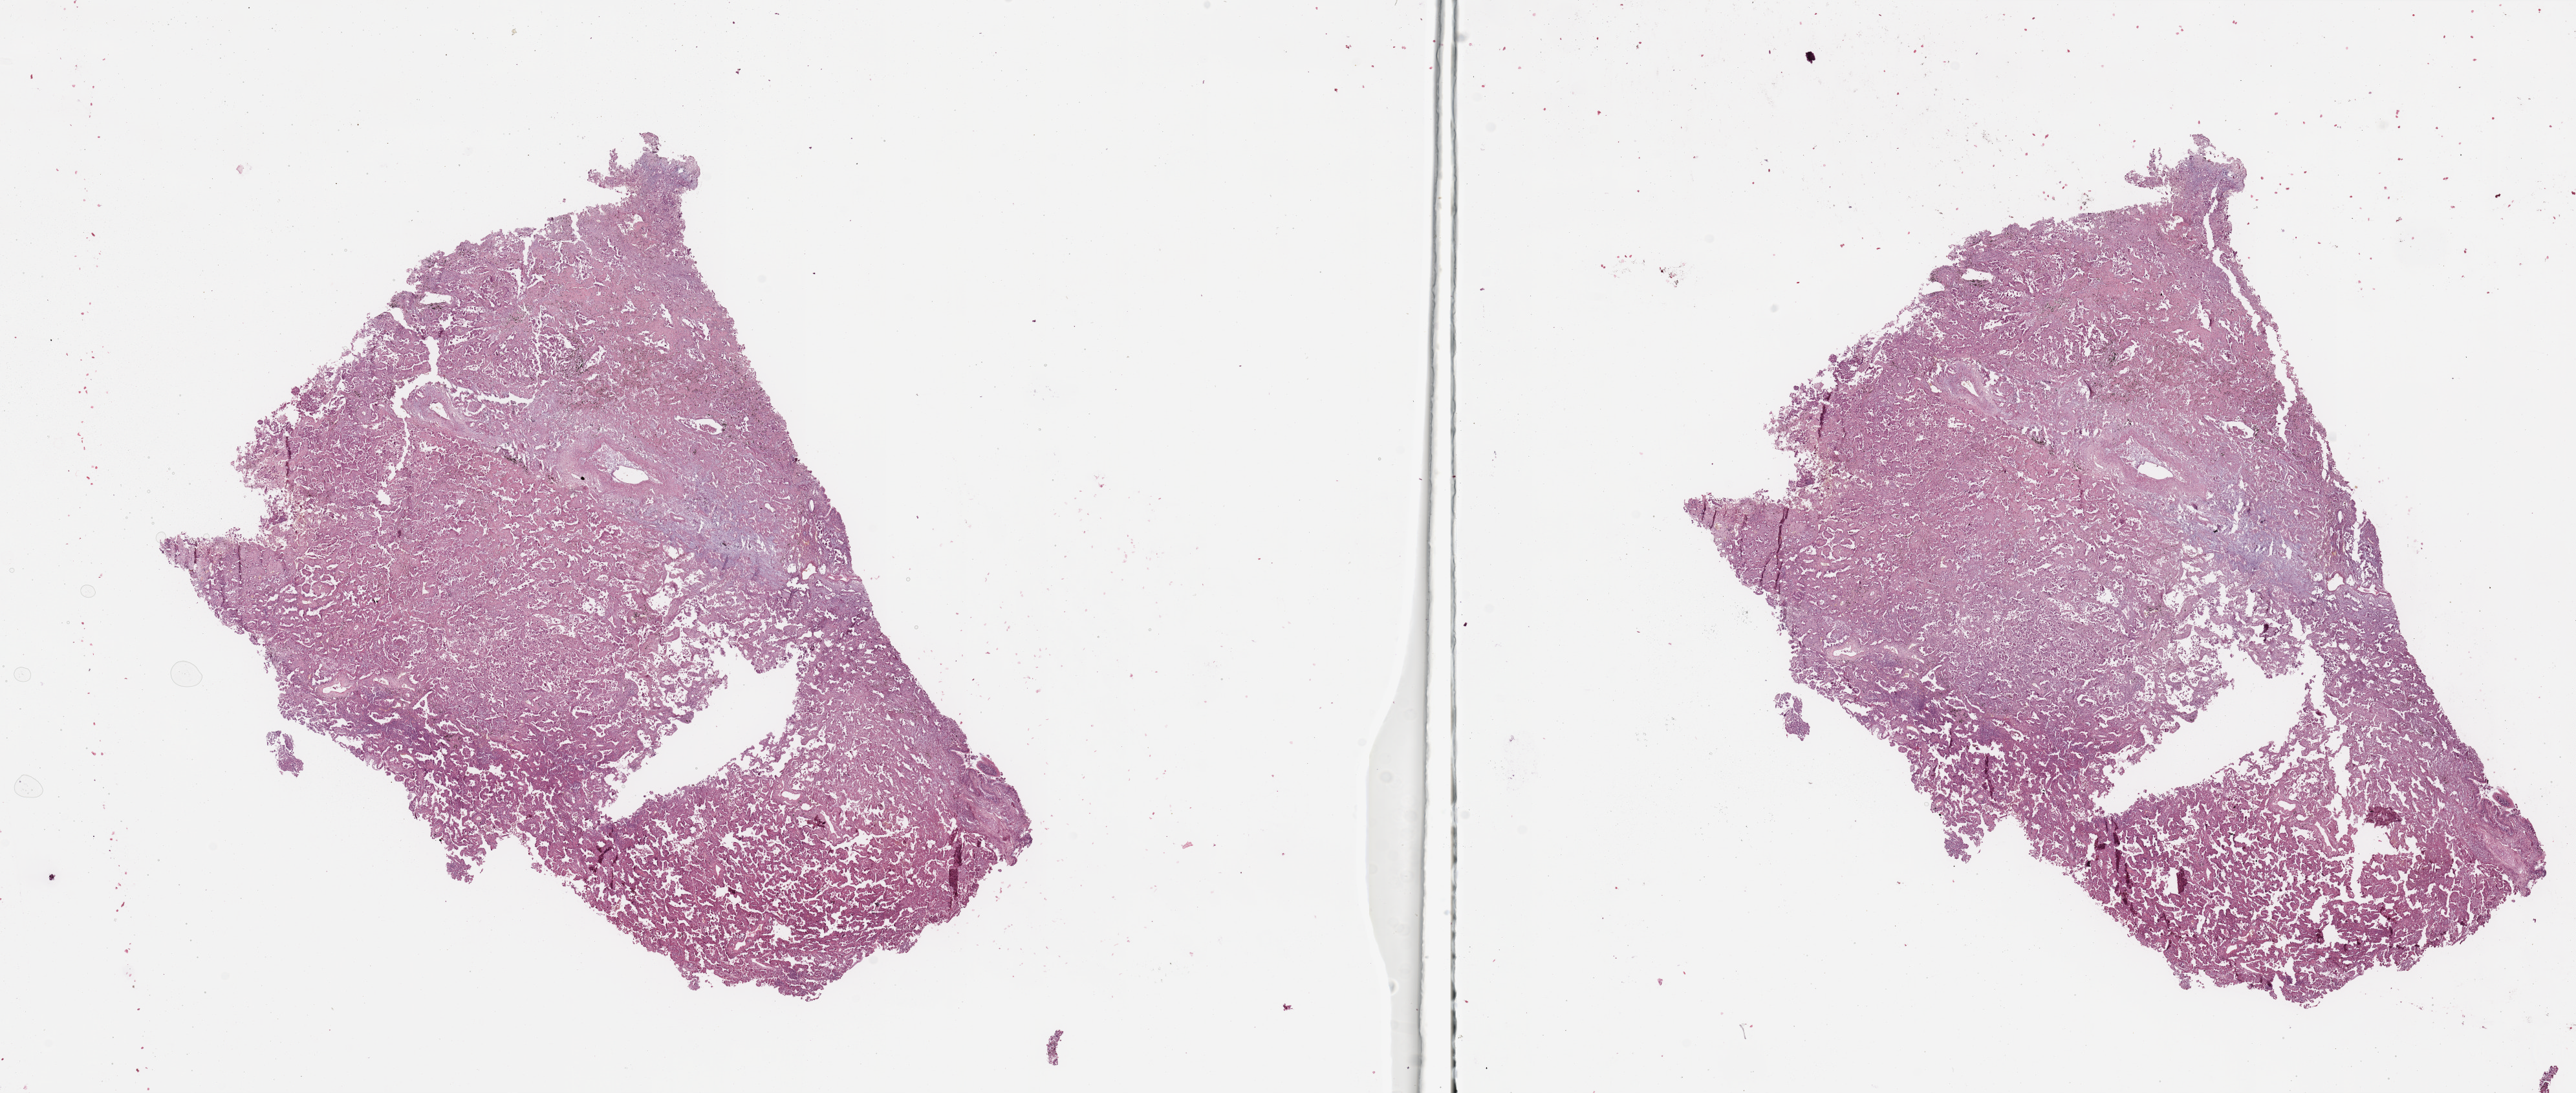
Hematoxylin and eosin (H&E) stained whole-slide image, shown as a low-resolution overview of the whole scanned area (about 31.5 x 13.4 mm). Tumour tissue sample, lung. Patient: male, age 56 years.
Diagnosis: Adenocarcinoma, NOS.